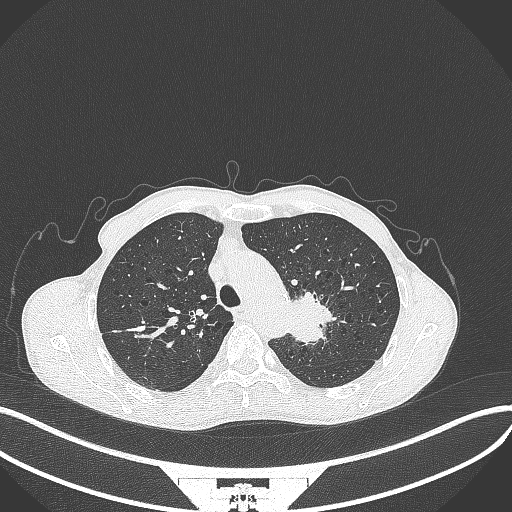
Chest CT, one axial slice. Position 315 of 386 along the scan axis. Reconstruction kernel B70f. Lung window (W 1500 / L -600 HU). 512 × 512 image matrix. Patient: male, 65 years. Case-level facts recorded for this patient, not image findings: clinical TNM (as recorded): T2b N0 M0; histopathological grade: G2.
Annotated regions visible in this slice (rectangle marked by the reading radiologist):
- lung tumour (recorded histology: adenocarcinoma): bounding box [x1, y1, x2, y2] px = [288, 287, 337, 349]